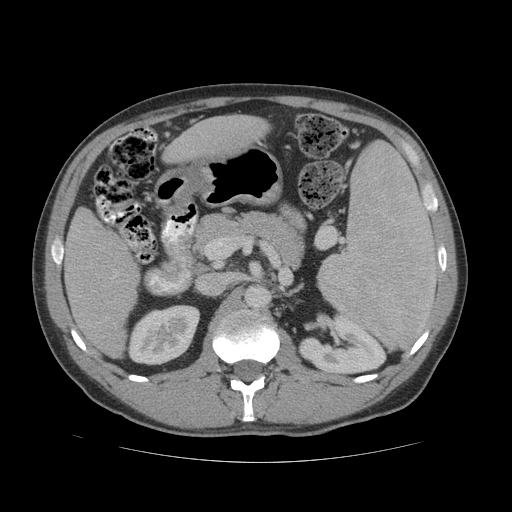
Contrast-enhanced abdominal CT (liver protocol), one axial slice. 140 kVp. Soft-tissue window (W 400 / L 40 HU). 2.5 mm slice thickness. 512 × 512 image matrix, field of view 400 × 400 mm. From the clinical record (not read from this slice): diagnosis: hepatocellular carcinoma (patient treated with transarterial chemoembolisation; whether this scan precedes or follows treatment is not stated here); TNM stage (as recorded): Stage-IVB; Child-Pugh class: B; tumour nodularity: multinodular.
Outlined on this slice (semi-automatic segmentation, software-assisted and operator-edited):
- liver parenchyma outside the tumour (the mass and vessels are separate outlines, so this box may not span the whole liver): box from (x=64, y=114) to (x=268, y=356) px
- liver vessels: (x=111, y=276)–(x=116, y=279)